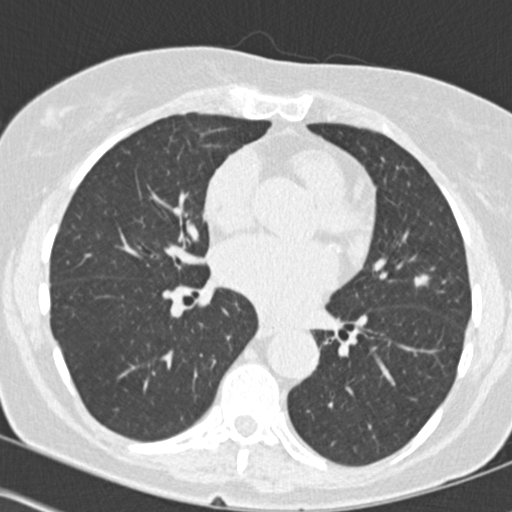
Low-dose screening chest CT, one axial slice. Slice 81 of 160 in the series (ordered by position). Reconstruction kernel B30f. 120 kVp. Lung window (W 1500 / L -600 HU). 2 mm slice thickness. 512 × 512 image matrix.
Annotated regions visible in this slice (outlined manually by an expert reader):
- lesion 1 (tumor, upper lobe of left lung): bounding box <415,275,428,286> (left, top, right, bottom; pixels)